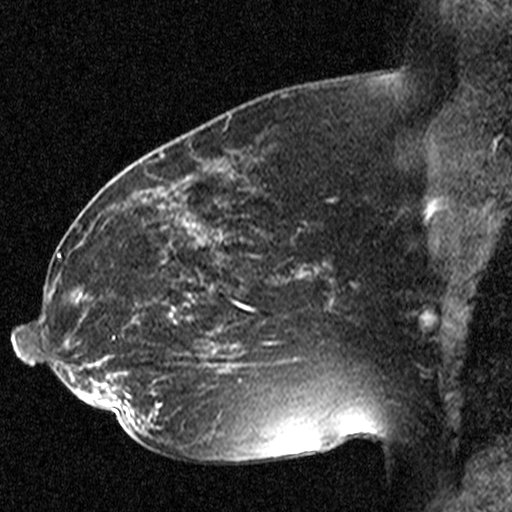
Breast MRI (dynamic contrast-enhanced), one sagittal slice. Slice 26 of 44 in the series (ordered by position). Dynamic contrast-enhanced study with each time point stored as its own series, time point 2 of 3 at this slice position (early post-contrast, ordered by acquisition time). 1.5 T. TE 4.5 ms, TR 11 ms. 3 mm slice thickness. 512 × 512 image matrix. Patient: female, 38 years. From the clinical record (not read from this slice): setting: breast cancer imaged before/during neoadjuvant chemotherapy; receptor status: HR-positive, HER2-negative.
Structures marked on this image (semi-automatically segmented with operator editing):
- analysis volume of interest (the breast-tissue region the enhancement analysis was run in; not a lesion): box from (x=176, y=272) to (x=251, y=349) px
- tumour enhancement mask (voxels above the 90 % enhancement threshold inside the analysis volume of interest): (x=183, y=275)–(x=251, y=321)